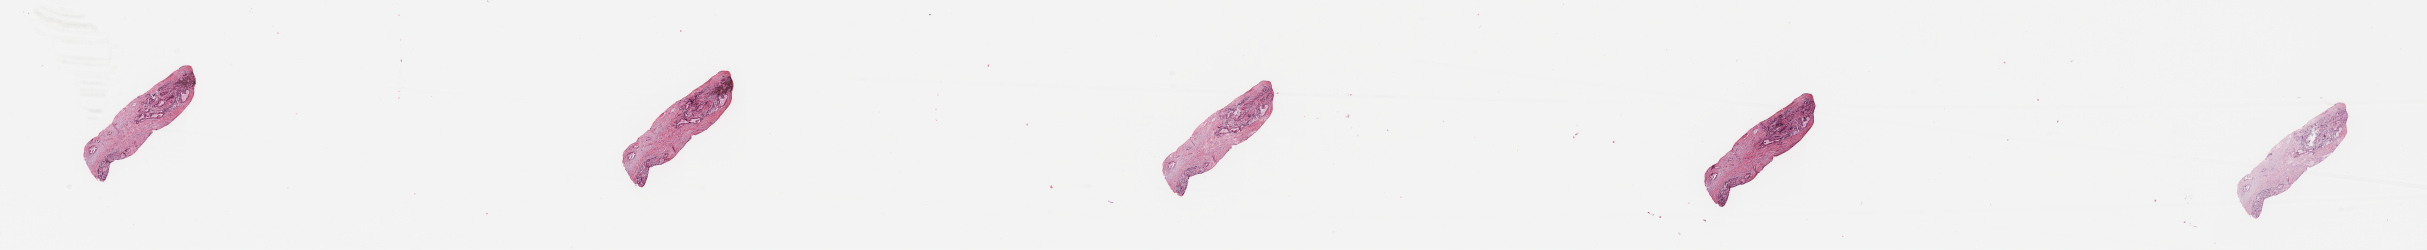
Hematoxylin and eosin (H&E) stained whole-slide image, low-resolution overview of the scanned area, about 38.4 x 4.0 mm (acquisition: 20x scan), tumour tissue sample, sampled site: pancreas. Patient: male, age 74 years. Histologic grade: G1 (well differentiated). Pathologist review of this section (percent, as recorded): tumour nuclei 30%, necrosis 0%.
Diagnosis: Infiltrating duct carcinoma, NOS. AJCC pathologic stage: IB.